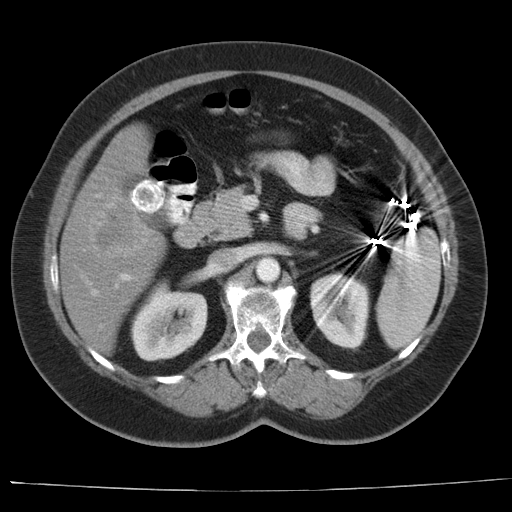
Contrast-enhanced abdominal CT, one axial slice; position 14 of 44 along the scan axis; 140 kVp; intravenous contrast given; soft-tissue window (W 400 / L 40 HU); 5 mm slice thickness; 512 × 512 image matrix. Female patient. From the clinical record (not read from this slice): diagnosis: colorectal cancer liver metastases, imaged before liver resection.
Annotated regions visible in this slice (outlined manually by an expert reader):
- hepatic veins: bounding box <91,289,96,296> (left, top, right, bottom; pixels)
- liver: <61,126,165,355>
- planned liver remnant (the part of the liver to remain after resection): <103,127,149,181>
- portal vein (with intrahepatic branches): <120,274,129,281>
- liver metastasis: <89,200,149,257>